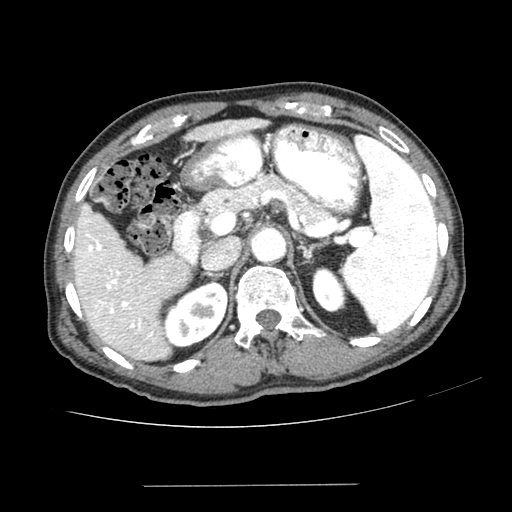
Contrast-enhanced abdominal CT (liver protocol), one axial slice. Position 149 of 187 along the scan axis. 100 kVp. One of 2 acquisitions stored at this slice position. Soft-tissue window (W 400 / L 40 HU). 2.5 mm slice thickness. 512 × 512 image matrix. From the clinical record (not read from this slice): diagnosis: hepatocellular carcinoma (patient treated with transarterial chemoembolisation; whether this scan precedes or follows treatment is not stated here); TNM stage (as recorded): Stage-I.
Annotated regions visible in this slice (semi-automatically segmented with operator editing):
- liver parenchyma outside the tumour (the mass and vessels are separate outlines, so this box may not span the whole liver): bounding box <74,118,266,360> (left, top, right, bottom; pixels)
- liver vessels: <84,126,258,337>